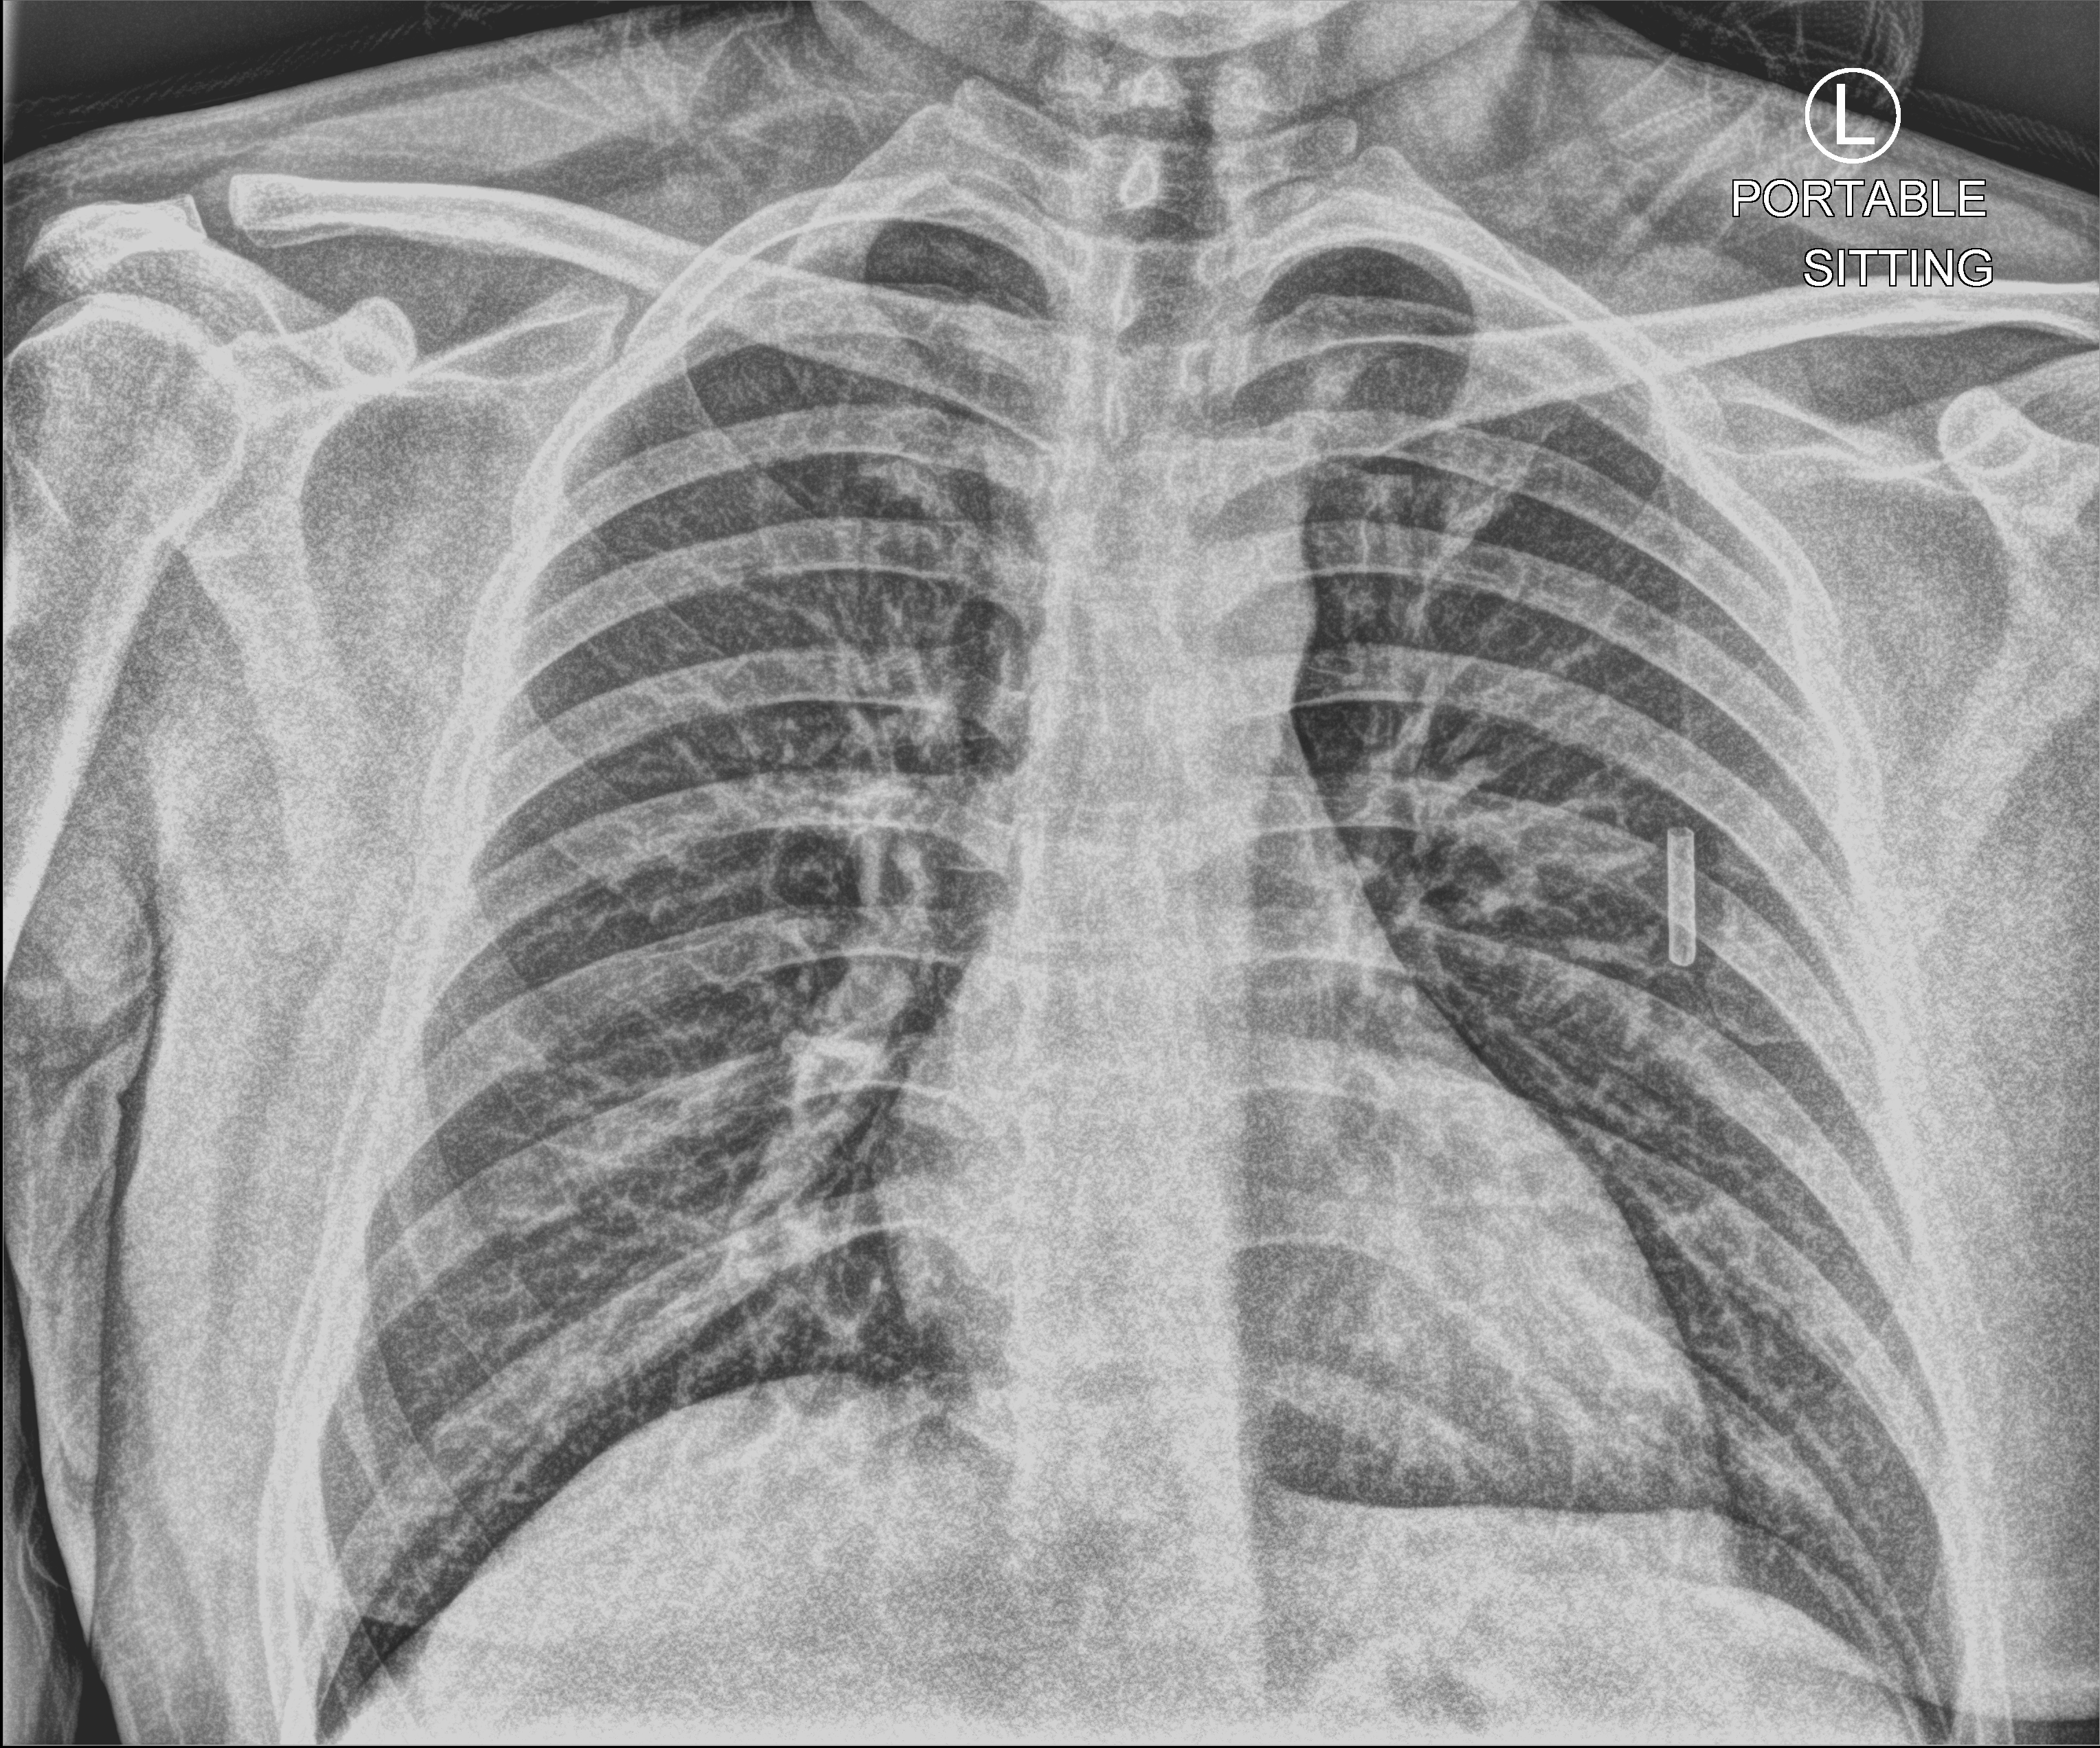
Chest X-ray (portable); anteroposterior (AP) projection. Male patient hospitalised with COVID-19, age 18–59 years.
Hospital-stay facts (about this admission, not read from this image; timing relative to this image not recorded): admitted to intensive care during this hospital stay: no.